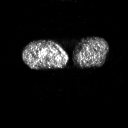
FDG PET of an extremity soft-tissue mass (from a PET/CT study), one axial slice; slice 235 of 311 in the series (ordered by position); 3.27 mm slice thickness; 128 × 128 image matrix, field of view 700 × 700 mm. Patient: male, 50 years. From the clinical record (not read from this slice): histological type: undifferentiated - pleiomorphic; grade: high; site of the primary tumour: right thigh.
Structures marked on this image (expert contour drawn on MRI and transferred to this co-registered scan by the dataset authors):
- gross tumour volume including surrounding oedema: bounding box <42,52,54,58> (left, top, right, bottom; pixels)